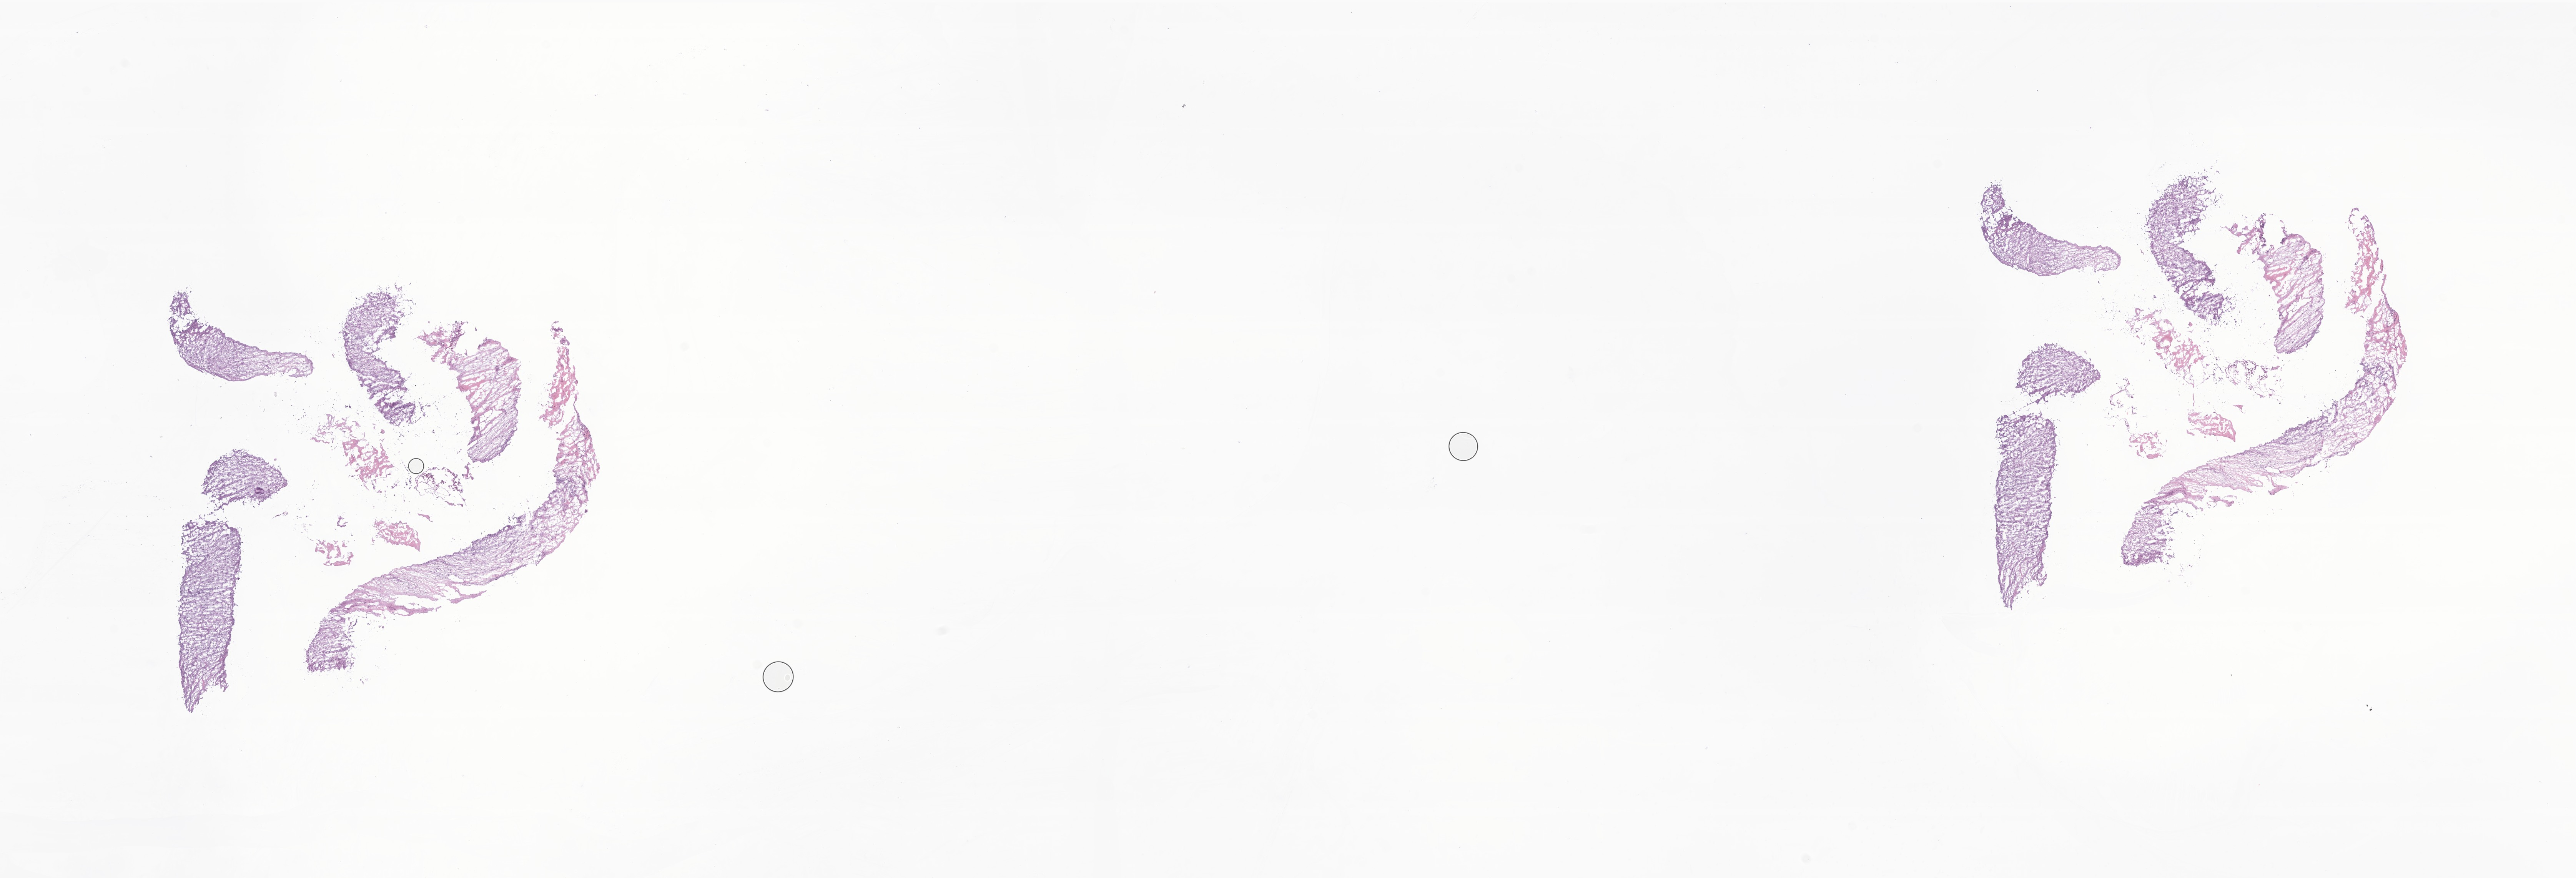
Whole-slide image, H&E stain of tumor tissue from the soft tissues of head and neck — whole scanned area (about 28.2 x 9.6 mm) shown as a low-resolution overview; frozen section (OCT-embedded). Patient female; age 182 months (15 years 2 months).
Diagnosis: Epithelioid sarcoma, NOS.